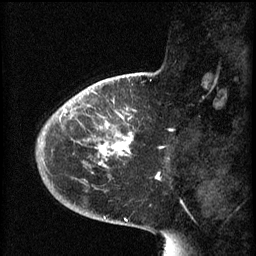
Breast MRI (dynamic contrast-enhanced), one sagittal slice; position 16 of 60 along the scan axis; 3 images stored at this slice position (order not interpretable as contrast timing); 1.5 T; TE 4.2 ms, TR 8.1 ms; 2 mm slice thickness; 256 × 256 image matrix, field of view 200 × 200 mm. Patient: female, 44 years.
Outlined on this slice (semi-automatically segmented with operator editing):
- analysis volume of interest (the breast-tissue region the enhancement analysis was run in; not a lesion): bounding box <59,110,136,167> (left, top, right, bottom; pixels)
- tumour enhancement mask (voxels above the 70 % enhancement threshold inside the analysis volume of interest): <59,110,133,167>